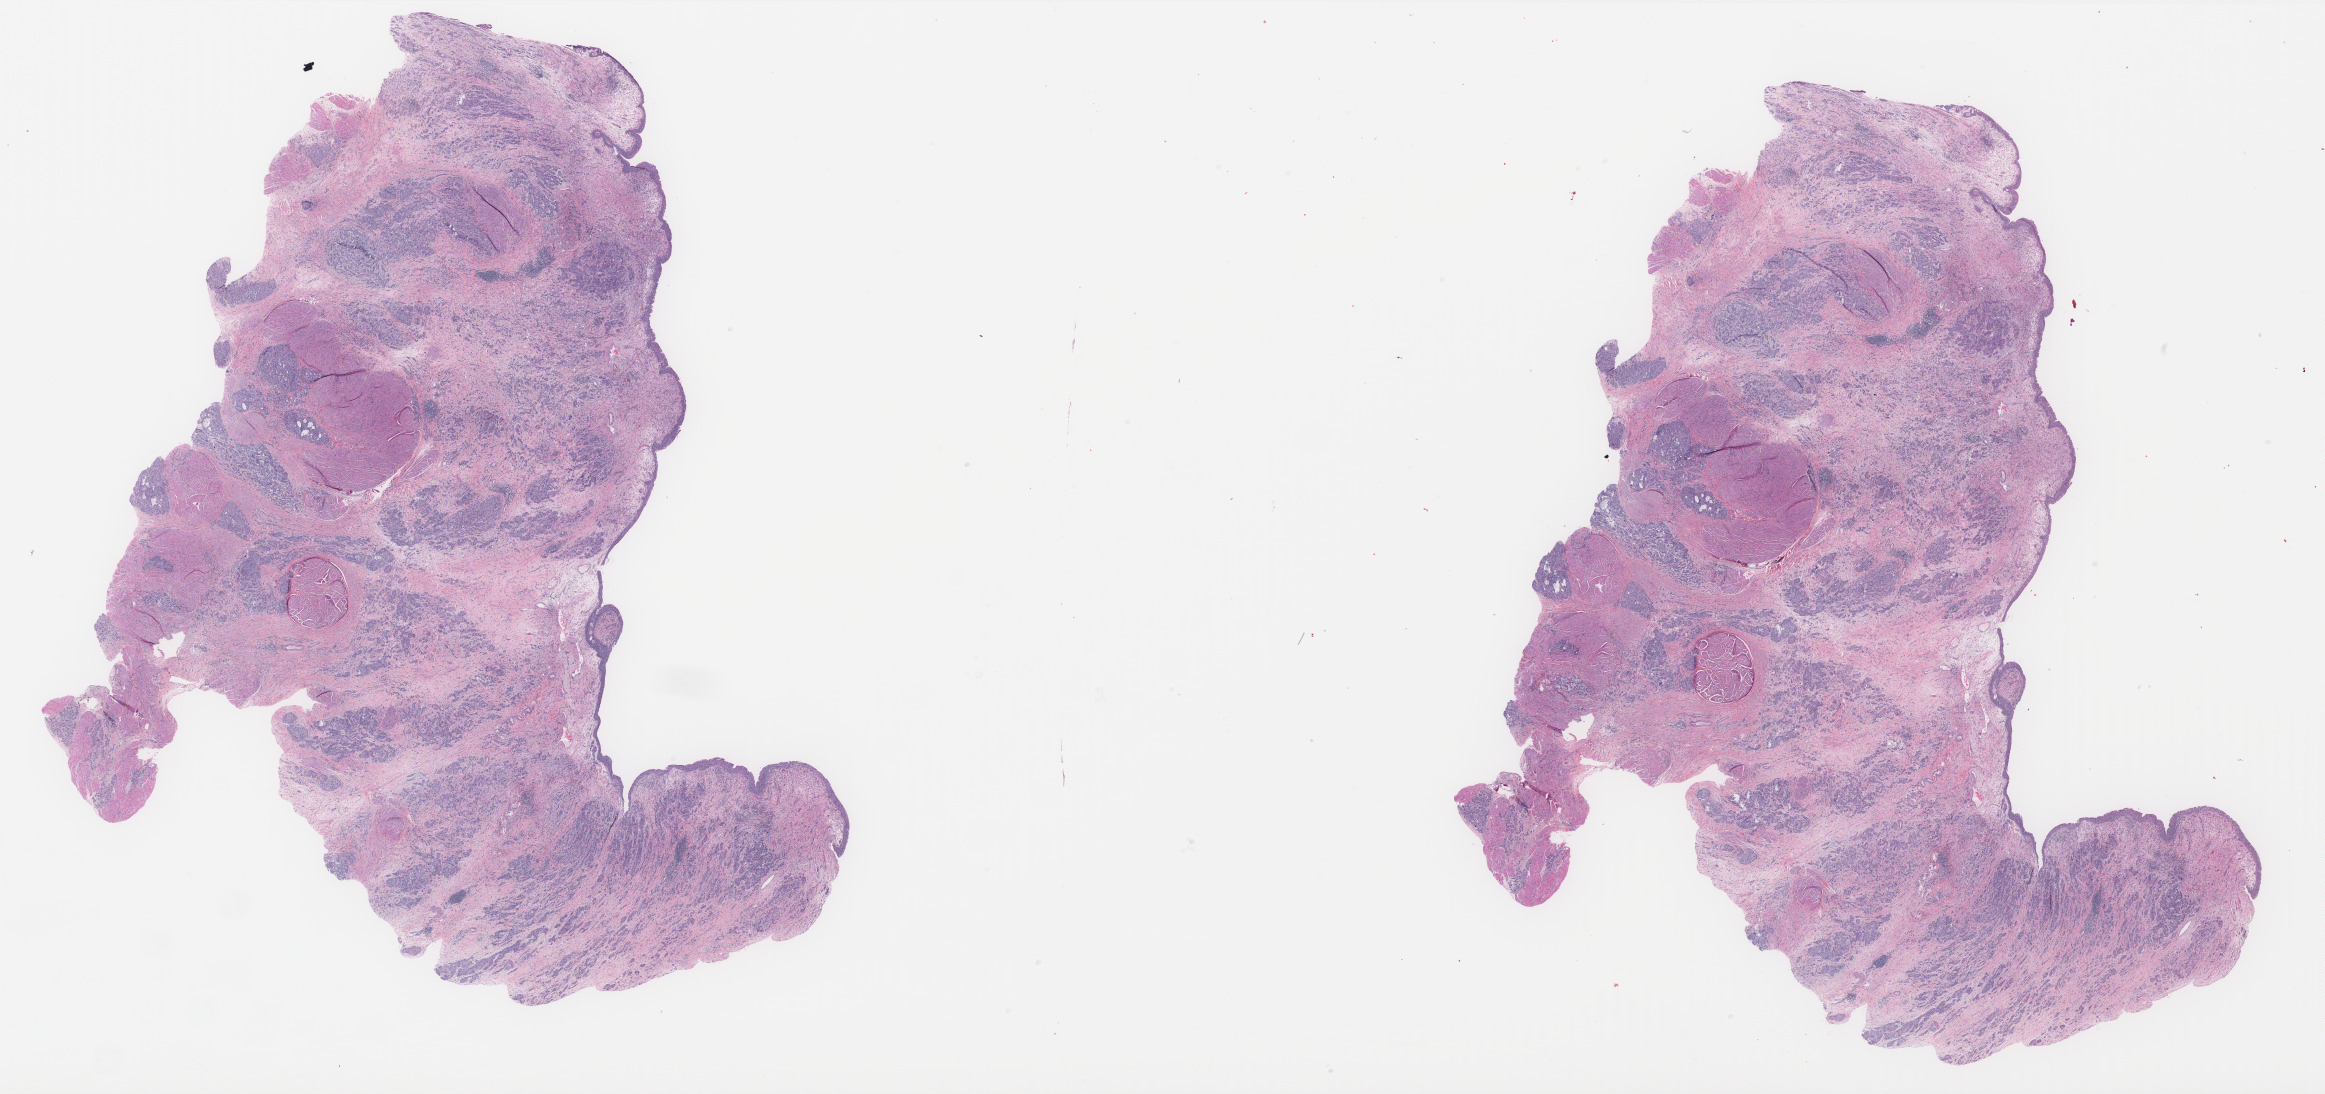
Digitized H&E tissue section (whole slide), shown as a low-resolution overview of the whole scanned area (about 37.3 x 17.5 mm). FFPE section. Sample: primary tumour, bladder. Male, age 84 years at initial diagnosis. Histologic grade: high grade.
AJCC pathologic stage: IV (6th edition). Diagnosis: Papillary transitional cell carcinoma. Lymph nodes positive (case pathology): 8 of 13 examined.